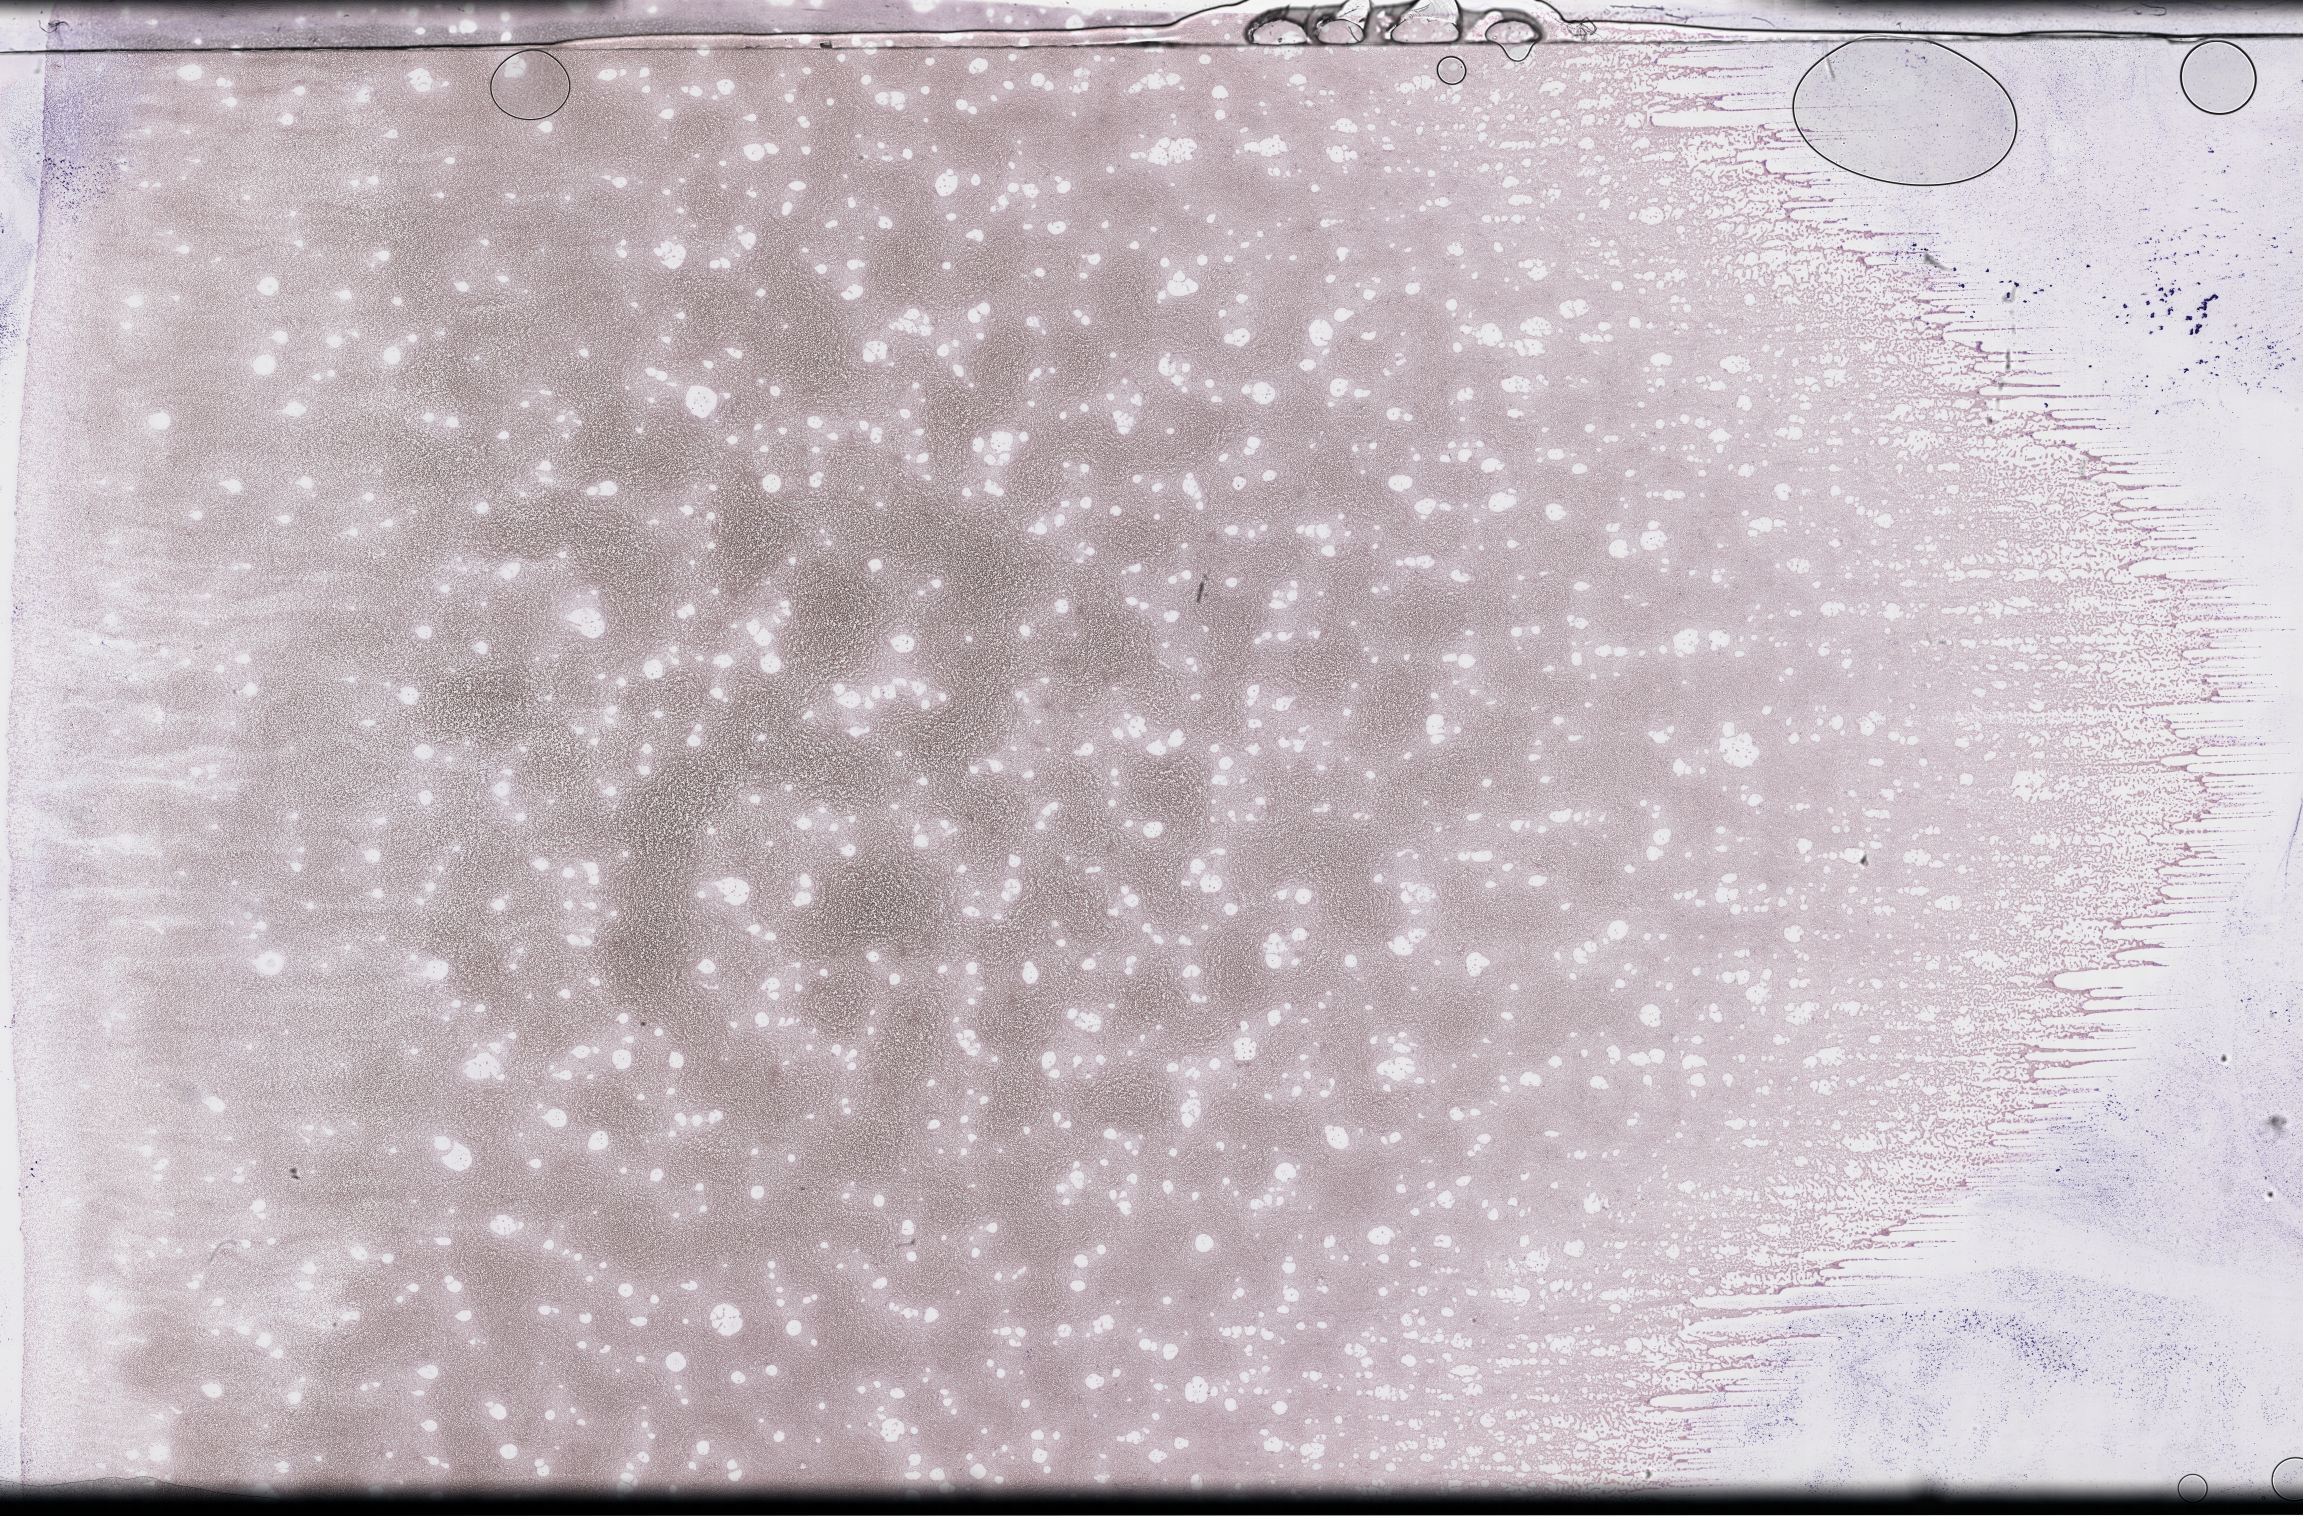
Whole-slide image of a whole blood smear, Wright–Giemsa stain, shown as a low-resolution overview of the whole scanned area (about 37.2 x 24.5 mm). EDTA-anticoagulated smear. Specimen time point: collected on treatment. Female patient.
Patient diagnosis: Plasma Cell Myeloma.